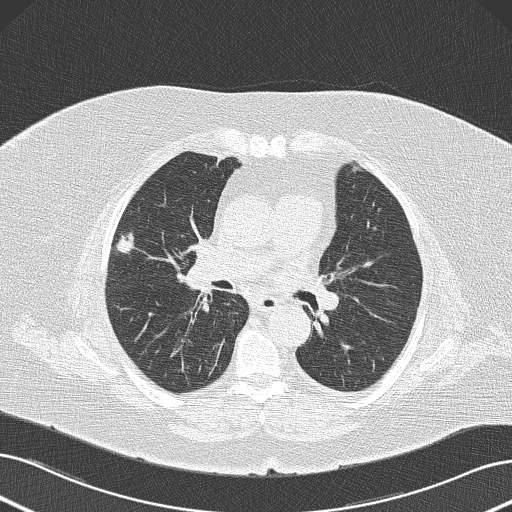
Low-dose screening chest CT, one axial slice; position 77 of 145 along the scan axis; lung window (W 1500 / L -600 HU); 512 × 512 image matrix, field of view 364 × 364 mm.
Annotated regions visible in this slice (outlined manually by an expert reader):
- lesion 1 (tumor, upper lobe of right lung): bounding box (x1, y1, x2, y2) in pixels: (115, 232, 134, 254)